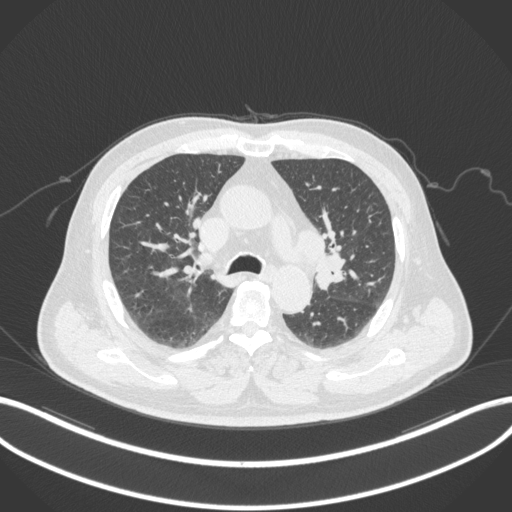
Chest CT, one axial slice. Slice 194 of 286 in the series (ordered by position). 120 kVp. Lung window (W 1500 / L -600 HU). 512 × 512 image matrix, field of view 400 × 400 mm. Patient: male, 67 years. Case-level facts recorded for this patient, not image findings: clinical TNM (as recorded): T2a N1 M0; histopathological grade: G3.
Annotated regions visible in this slice (rectangle marked by the reading radiologist):
- lung tumour (recorded histology: adenocarcinoma): bounding box <315,250,348,292> (left, top, right, bottom; pixels)